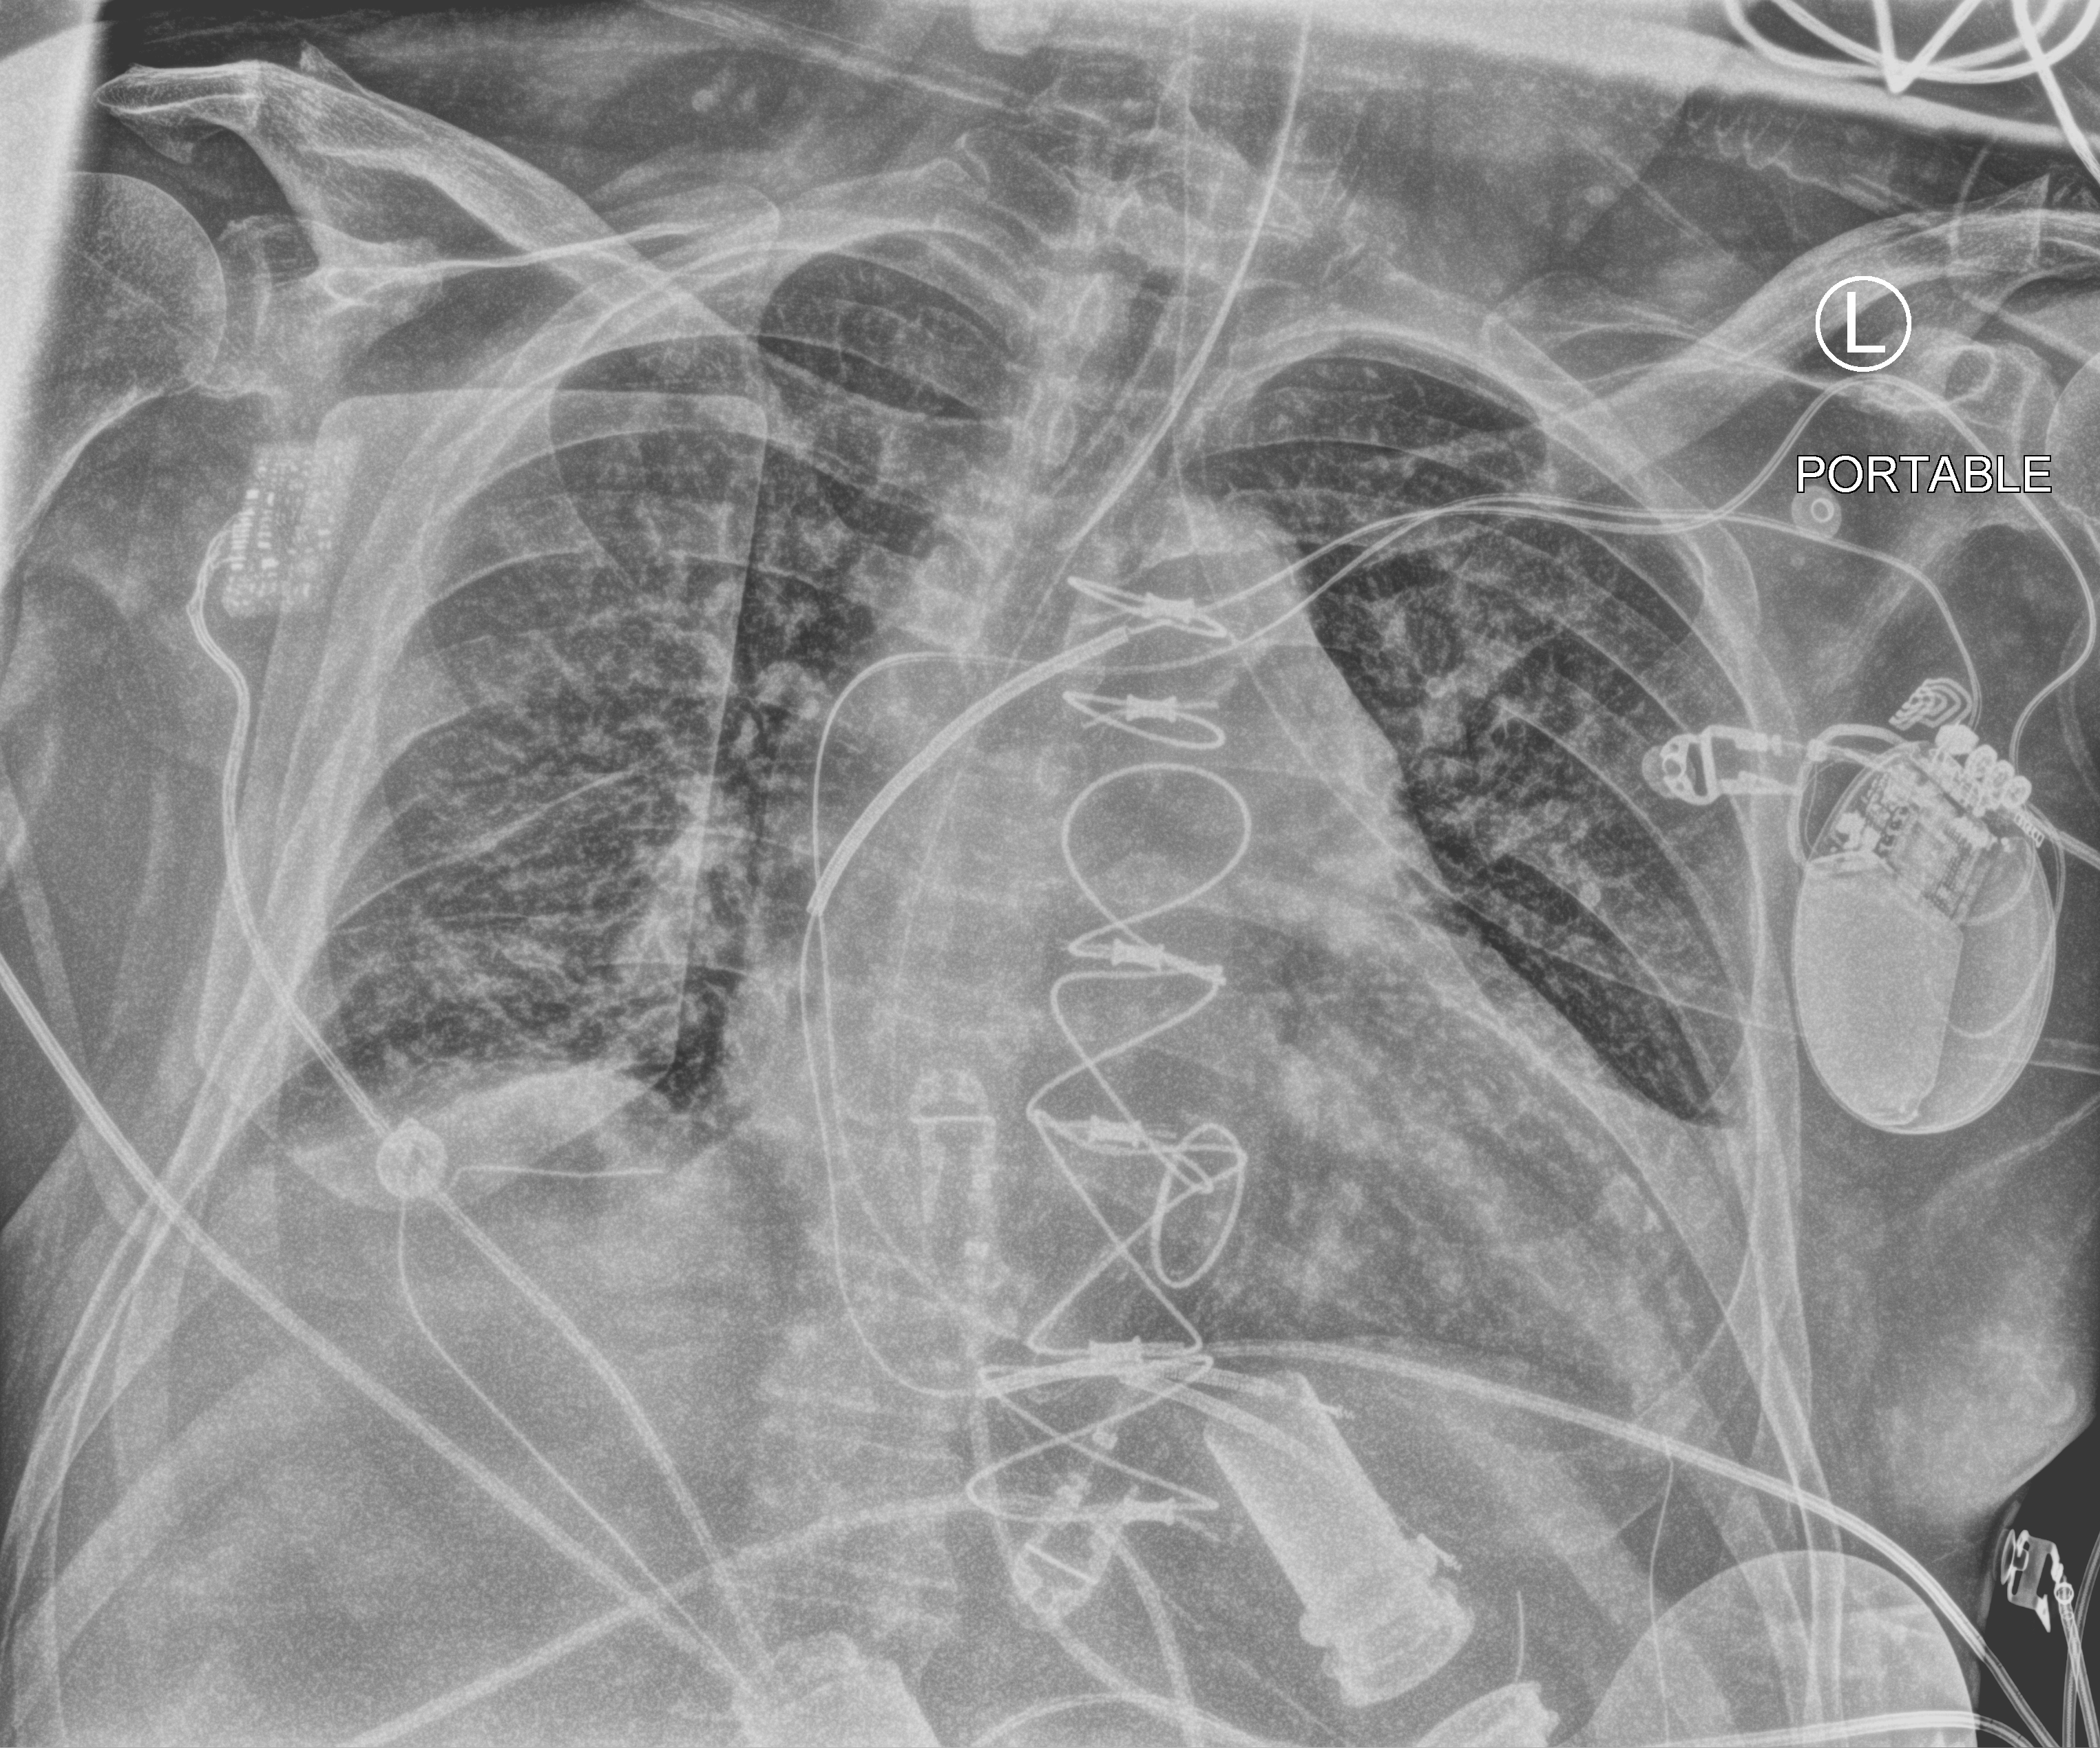
Portable chest radiograph, anteroposterior (AP) projection. Male patient hospitalised with COVID-19, age 60–74 years.
Admission-level facts for this patient (not findings on this image; timing relative to this image not recorded):
- mechanically ventilated during this hospital stay: no
- admitted to intensive care during this hospital stay: yes